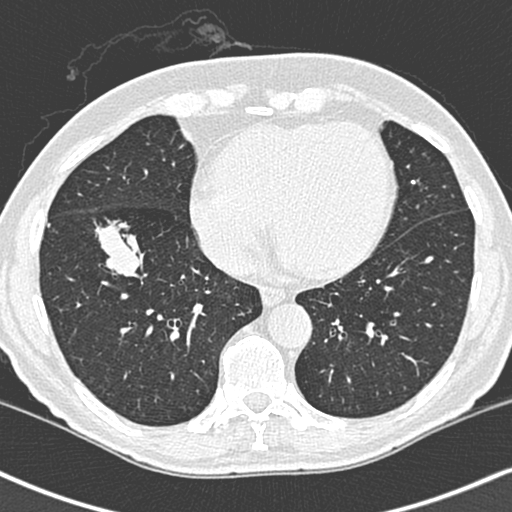
Low-dose screening chest CT, one axial slice. Slice 96 of 248 in the series (ordered by position). 120 kVp. Lung window (W 1500 / L -600 HU). 1.3 mm slice thickness. 512 × 512 image matrix.
Structures marked on this image (manually delineated by an expert):
- lesion 1 (tumor, lower lobe of right lung): bounding box [x1, y1, x2, y2] px = [95, 181, 141, 239]